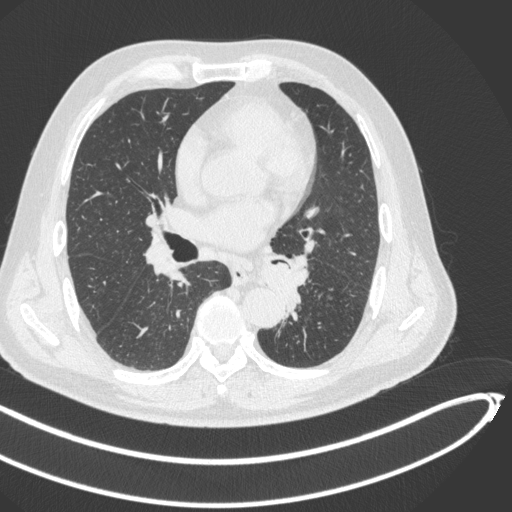
Chest CT, one axial slice. Reconstruction kernel B31f. 120 kVp. Lung window (W 1500 / L -600 HU). 512 × 512 image matrix, field of view 400 × 400 mm. Patient: male, 64 years. From the clinical record (not read from this slice): clinical TNM (as recorded): T1c N0 M0; histopathological grade: G2.
Structures marked on this image (rectangle marked by the reading radiologist):
- lung tumour (recorded histology: squamous cell carcinoma): bounding box [x1, y1, x2, y2] px = [258, 253, 302, 308]